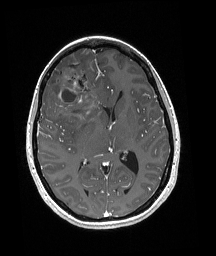
Brain MRI from a brain-tumour surgery series, one axial slice. Position 94 of 192 along the scan axis. T1-weighted post-contrast. 1 mm slice thickness. 216 × 256 image matrix, field of view 211 × 250 mm. Case-level facts recorded for this patient, not image findings: histopathology: Oligodendroglioma; WHO grade: 3; IDH mutation: yes; tumour location: Right Frontal.
Structures marked on this image (manually delineated by an expert):
- tumour: bounding box <51,60,98,119> (left, top, right, bottom; pixels)